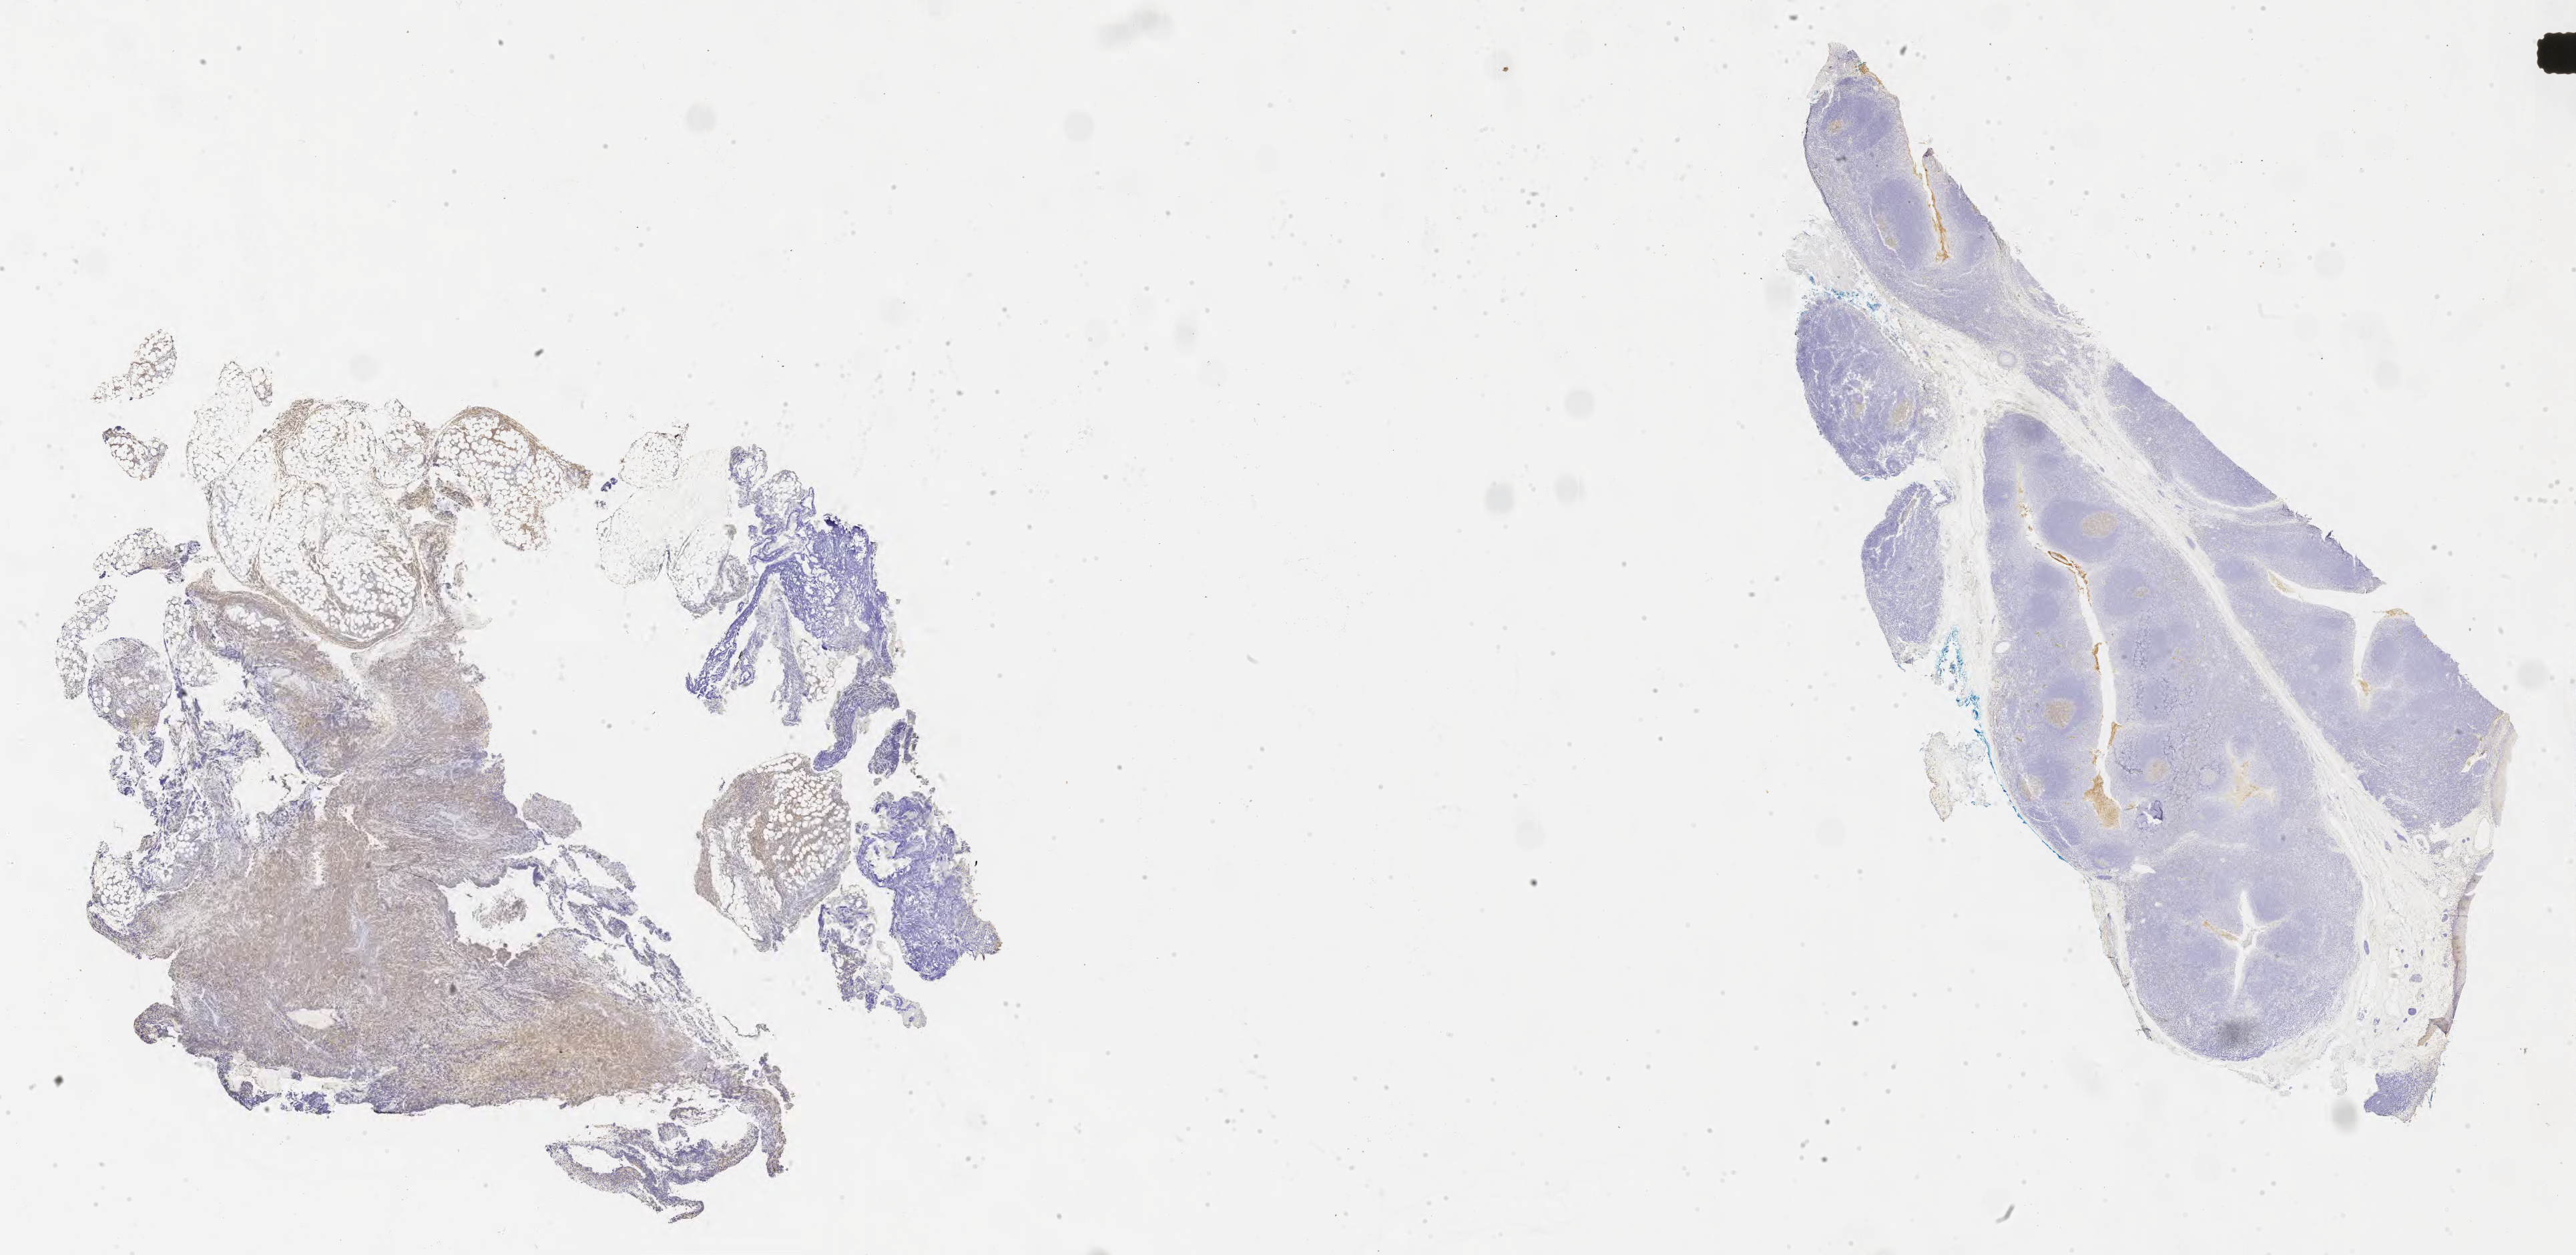
Immunohistochemistry (IHC) whole-slide image stained for CD10 — a low-resolution overview of the entire scanned area, about 31.2 x 15.2 mm; tumor tissue; site: abdominal lymph node. Patient: male, age at initial diagnosis 9 years.
* histologic diagnosis: Burkitt lymphoma, NOS